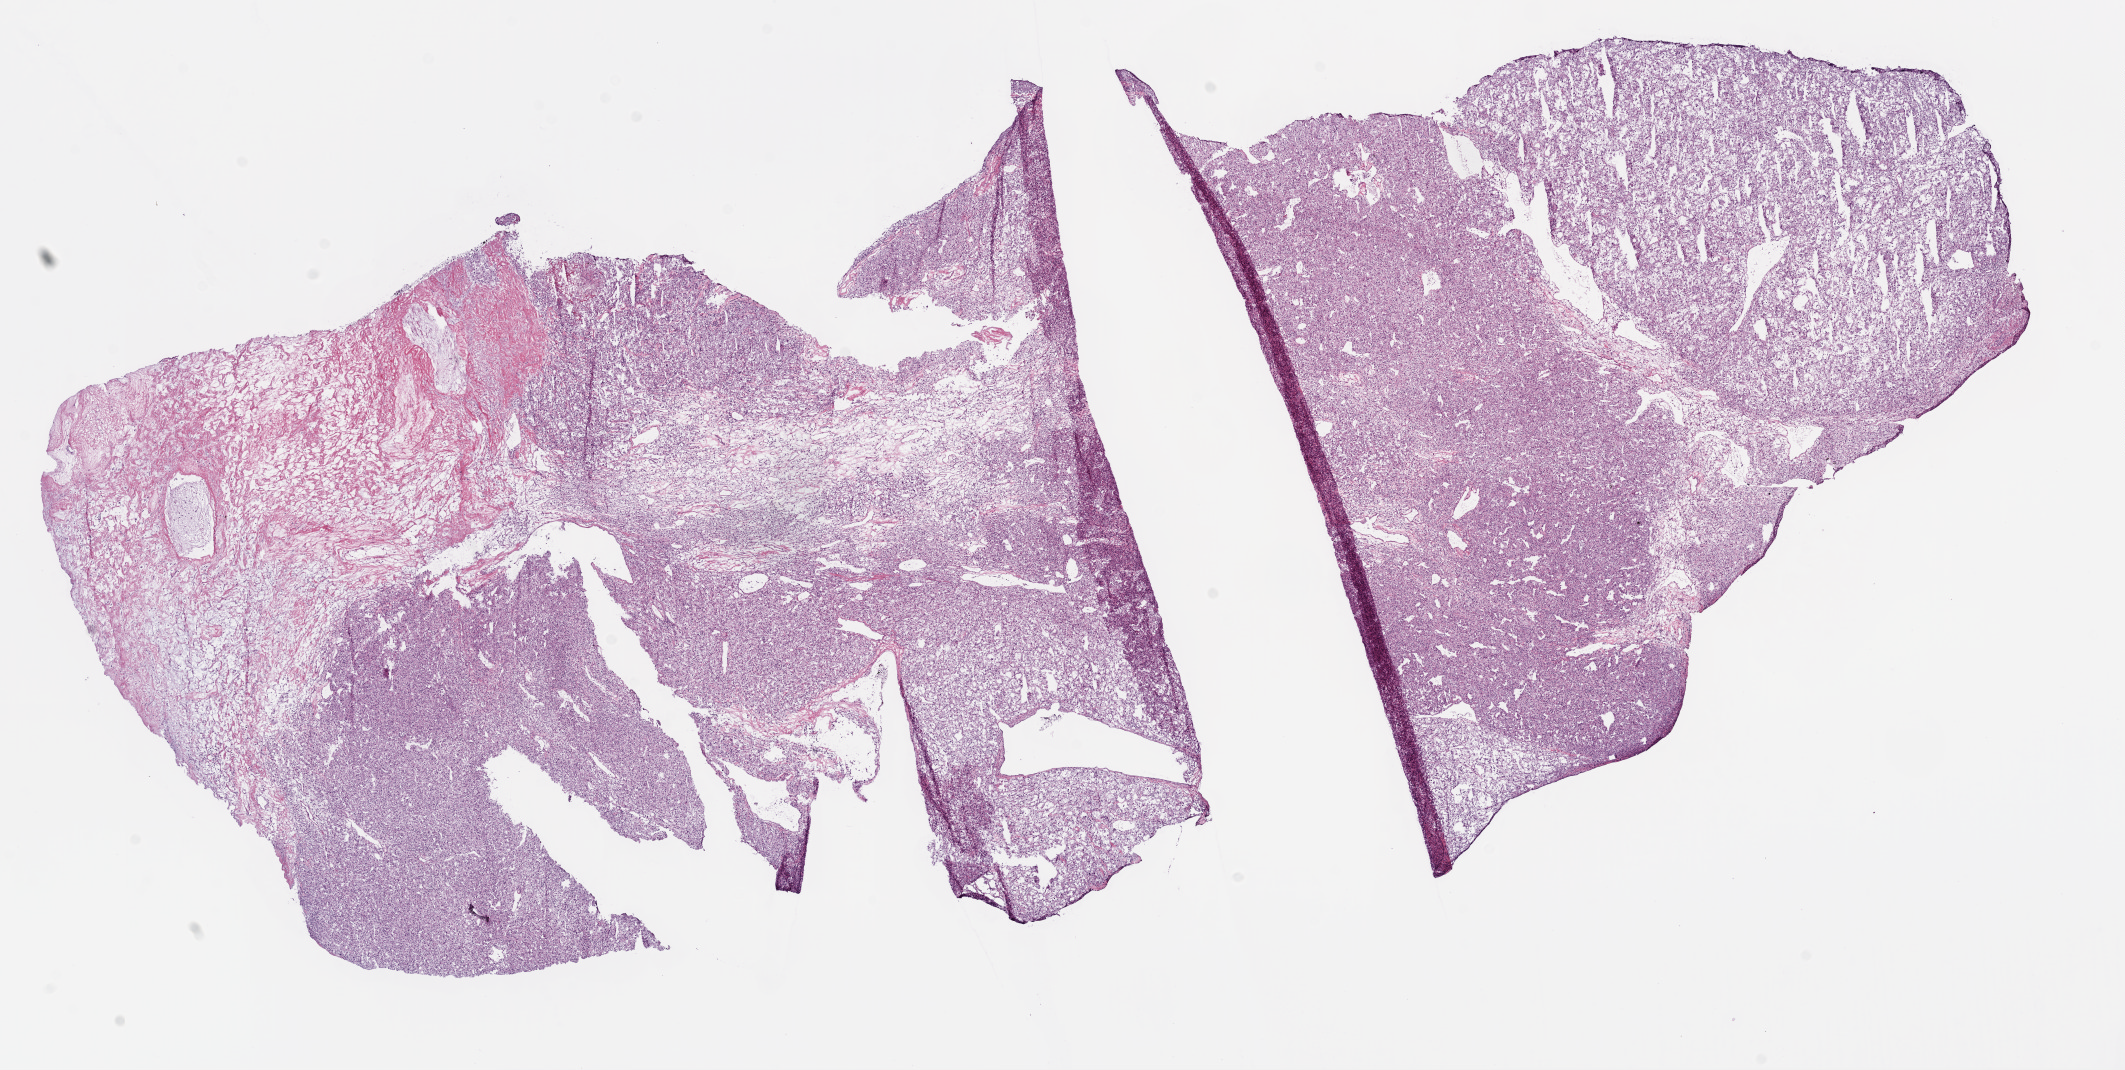
H&E-stained whole-slide image, a low-resolution overview of the entire scanned area, about 17.1 x 8.6 mm (acquisition: 20x scan), frozen section from the bottom of the tissue portion, kidney, primary tumour sample. Patient: male, age at initial diagnosis 60 years. Histologic grade: G4 (undifferentiated). Composition of this section per pathologist review: tumour cells 80%, tumour nuclei 80%, normal cells 0%, stromal cells 20%, necrosis 0%.
Laterality: right. Pathologic diagnosis: Clear cell adenocarcinoma, NOS. AJCC pathologic stage: I.